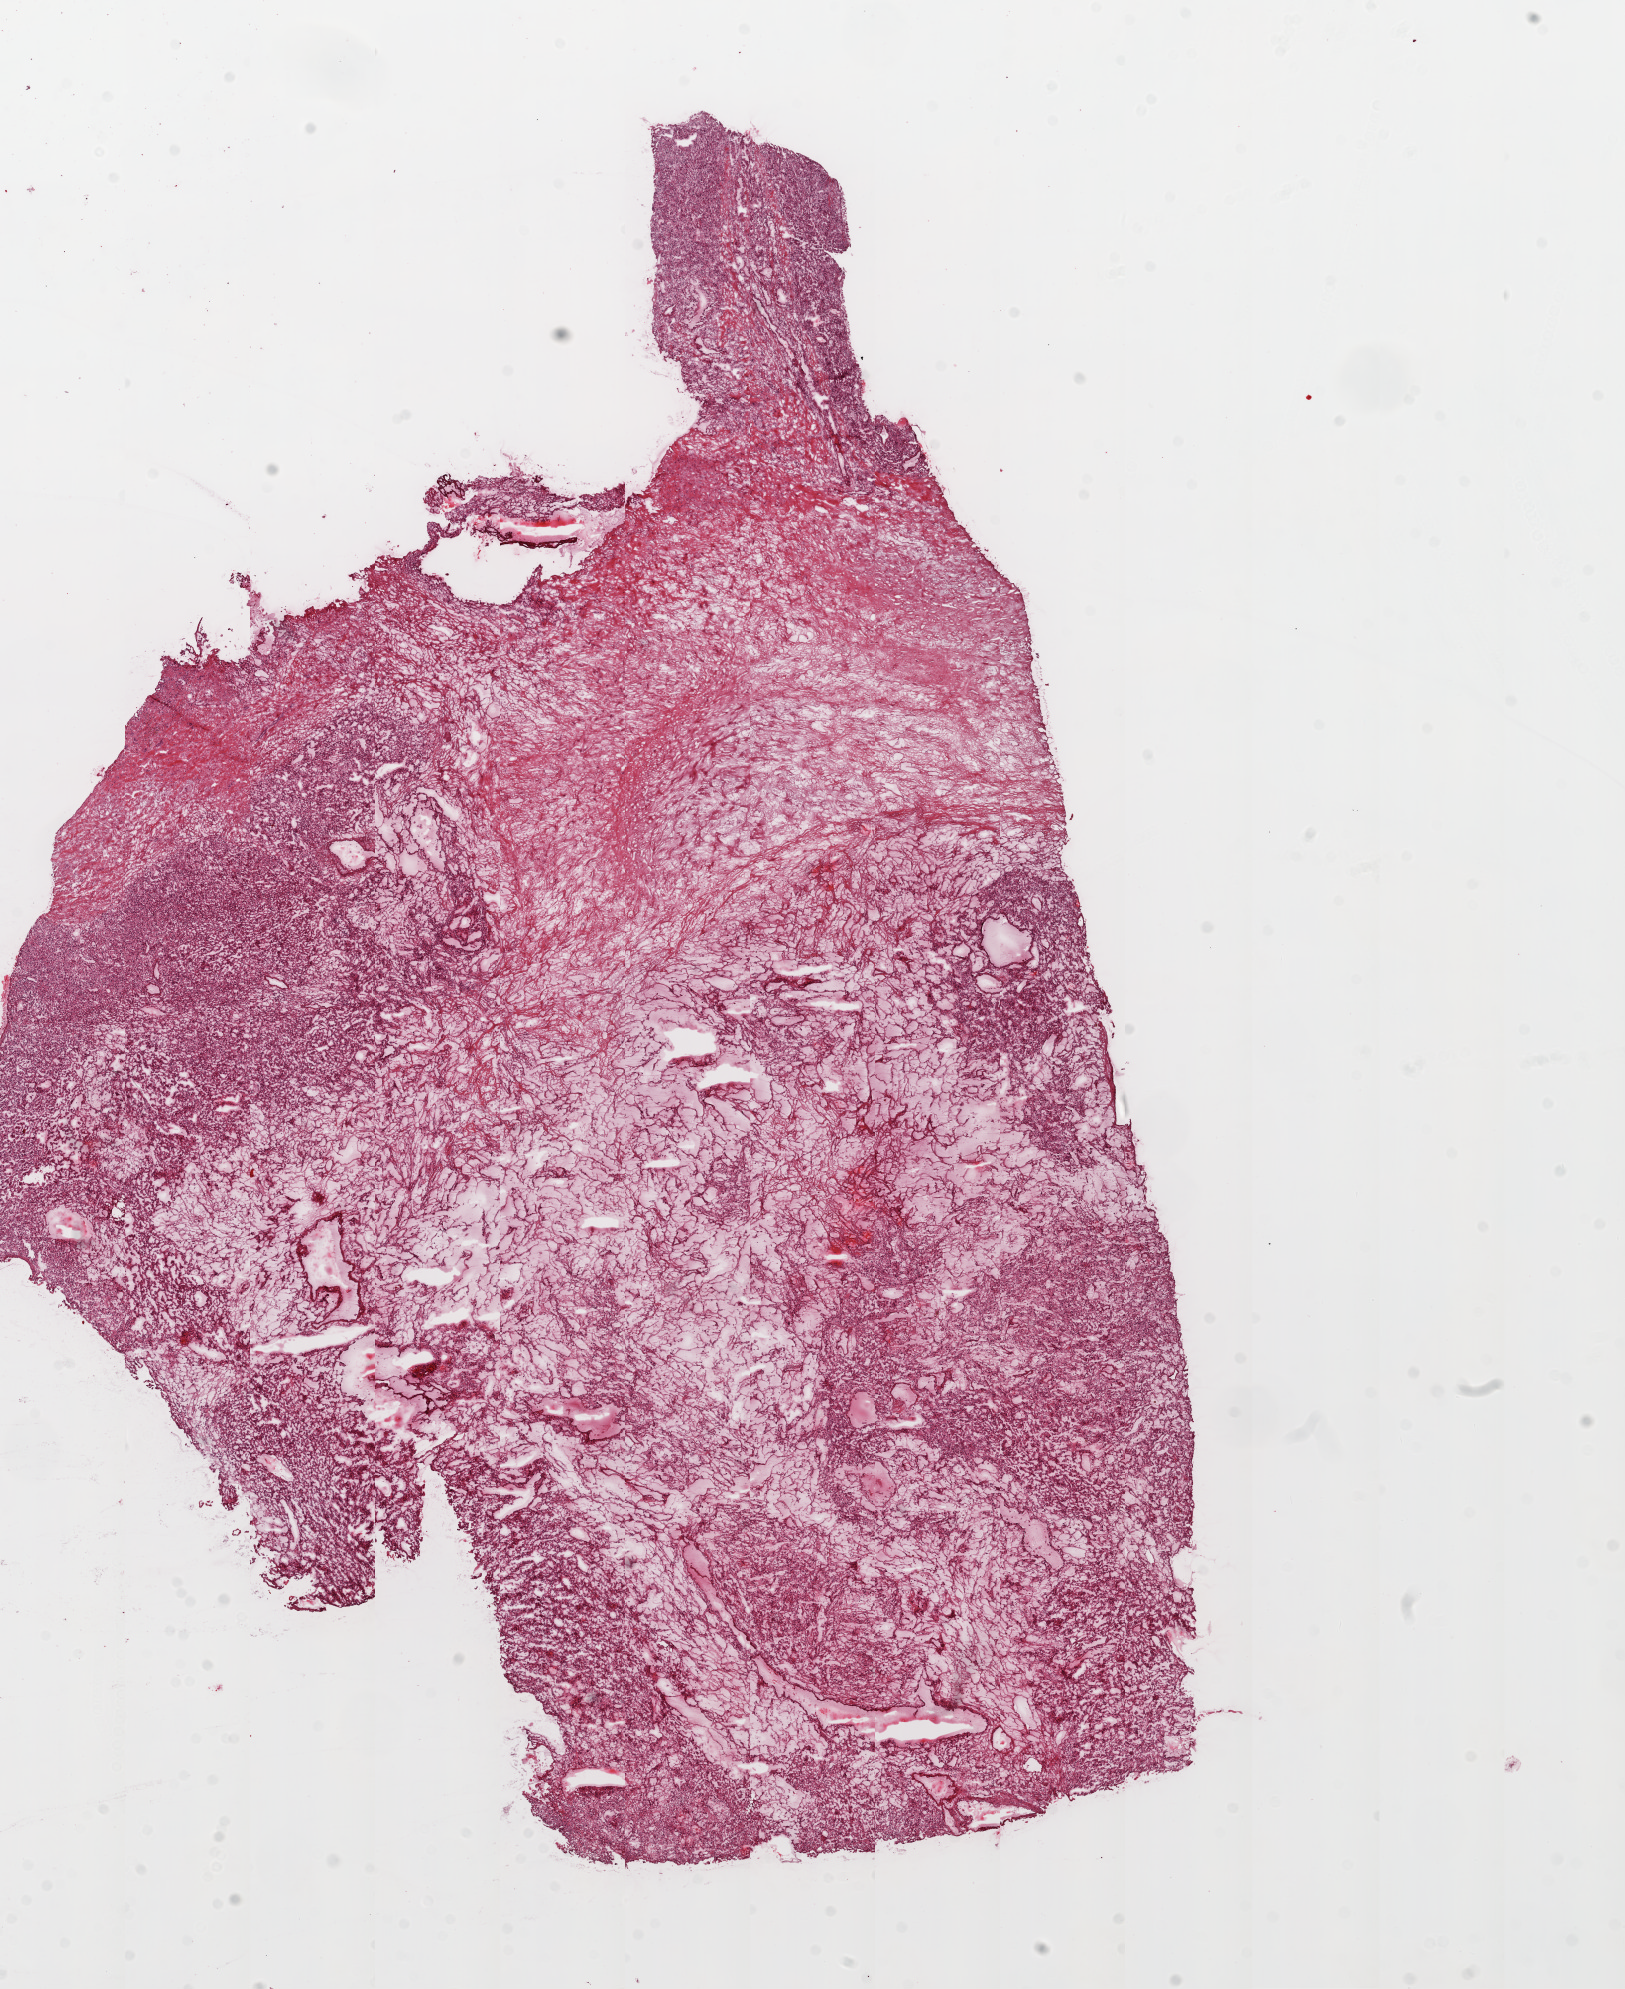
Whole-slide histology image, Hematoxylin and eosin (H&E) stained — shown as a low-resolution overview of the whole scanned area (about 13.0 x 16.0 mm, slide scanned at 20x); frozen section from the top of the tissue portion; primary tumour sample from the kidney. Male patient; age at initial diagnosis 44 years. Histologic grade: G3 (poorly differentiated). Slide review estimates, as recorded: tumour cells 85%, tumour nuclei 80%, normal cells 0%, stromal cells 15%, necrosis 0%.
AJCC pathologic stage: III. Pathologic diagnosis: Clear cell adenocarcinoma, NOS. Lymph nodes positive (case pathology): 2 of 2 examined.